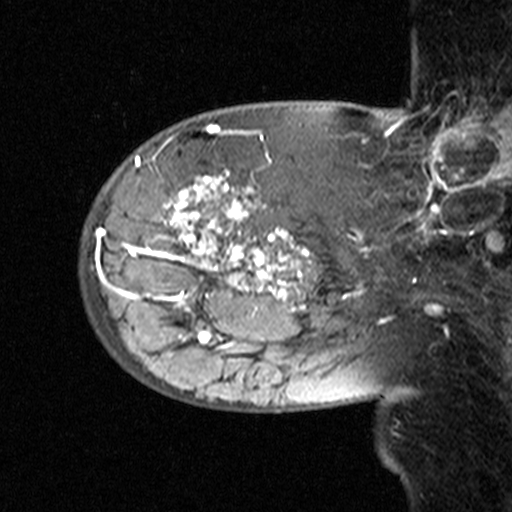
Breast MRI (dynamic contrast-enhanced), one sagittal slice. Position 12 of 44 along the scan axis. Dynamic contrast-enhanced study with each time point stored as its own series, time point 2 of 3 at this slice position (early post-contrast, ordered by acquisition time). 1.5 T. TE 4.5 ms, TR 11 ms. 3 mm slice thickness. 512 × 512 image matrix, field of view 200 × 200 mm. Patient: female, 53 years. Case-level facts recorded for this patient, not image findings: setting: breast cancer imaged before/during neoadjuvant chemotherapy; receptor status: HR-positive, HER2-negative.
Annotated regions visible in this slice (semi-automatic segmentation, software-assisted and operator-edited):
- analysis volume of interest (the breast-tissue region the enhancement analysis was run in; not a lesion): bounding box [x1, y1, x2, y2] px = [78, 140, 311, 353]
- tumour enhancement mask (voxels above the 90 % enhancement threshold inside the analysis volume of interest): [97, 140, 309, 342]